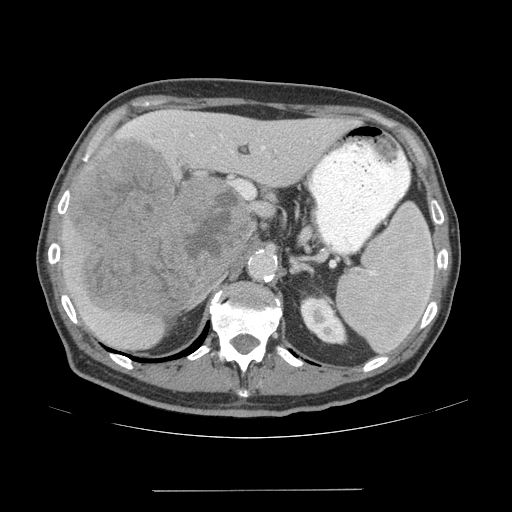
Contrast-enhanced abdominal CT (liver protocol), one axial slice. 140 kVp. Soft-tissue window (W 400 / L 40 HU). 2.5 mm slice thickness. 512 × 512 image matrix, field of view 400 × 400 mm. From the clinical record (not read from this slice): diagnosis: hepatocellular carcinoma (patient treated with transarterial chemoembolisation; whether this scan precedes or follows treatment is not stated here); TNM stage (as recorded): Stage-IVA; Child-Pugh class: A; tumour differentiation: well differentiated; tumour nodularity: uninodular.
Structures marked on this image (semi-automatic segmentation, software-assisted and operator-edited):
- liver parenchyma outside the tumour (the mass and vessels are separate outlines, so this box may not span the whole liver): box from (x=62, y=108) to (x=358, y=350) px
- mass: (x=68, y=141)–(x=252, y=316)
- liver vessels: (x=122, y=115)–(x=265, y=150)